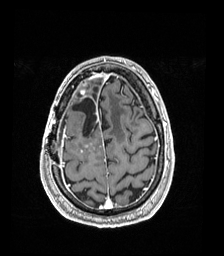
Brain MRI from a brain-tumour surgery series, one axial slice; T1-weighted post-contrast; 1 mm slice thickness; 224 × 256 image matrix, field of view 224 × 256 mm. From the clinical record (not read from this slice): histopathology: Astrocytoma; WHO grade: 4; IDH mutation: yes.
Annotated regions visible in this slice (outlined manually by an expert reader):
- previous resection cavity: box from (x=72, y=98) to (x=97, y=137) px
- tumour: (x=79, y=83)–(x=88, y=153)